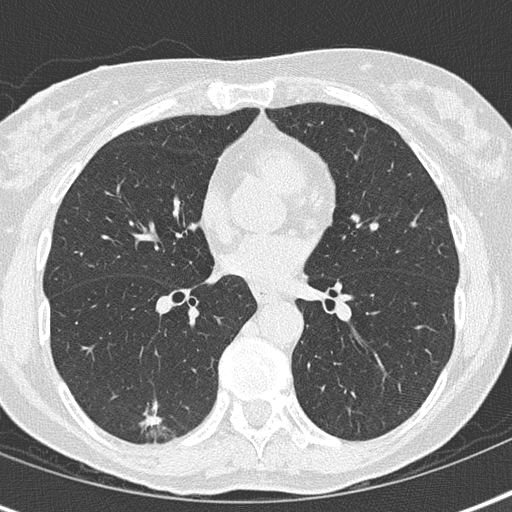
Axial slice from a low-dose chest CT screening exam, baseline screening round, lung window (W 1500 / L -600 HU), 2 mm slice thickness, lung (sharp) reconstruction kernel (B50f), slice 86 of 155 in the series, 512 × 512 image matrix, field of view 290 × 290 mm. Female, age 69 years at enrolment. Current smoker at enrolment.
Lesion marked by an expert reader, bounding box [x1, y1, x2, y2] px = [117, 397, 180, 454]. The screening reader recorded 2 non-calcified nodules or masses ≥4 mm on this exam (right lower lobe, left lower lobe); which of them this box marks is not recorded. Official screen result: positive, change unspecified: nodule(s) >= 4 mm or enlarging nodule(s), mass(es), or other non-specific abnormalities suspicious for lung cancer.